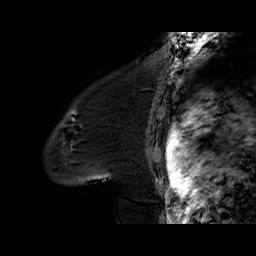
Breast MRI (dynamic contrast-enhanced), one sagittal slice; position 50 of 60 along the scan axis; dynamic contrast-enhanced series, time point 2 of 6 at this slice position (early post-contrast); 1.5 T; TE 6.2 ms, TR 32.4 ms; 256 × 256 image matrix, field of view 200 × 200 mm. Female patient. From the clinical record (not read from this slice): setting: breast cancer imaged before/during neoadjuvant chemotherapy; receptor status: triple-negative.
Structures marked on this image (semi-automatically segmented with operator editing):
- analysis volume of interest (the breast-tissue region the enhancement analysis was run in; not a lesion): bounding box <45,97,134,185> (left, top, right, bottom; pixels)
- tumour enhancement mask (voxels above the 100 % enhancement threshold inside the analysis volume of interest): <71,119,73,146>